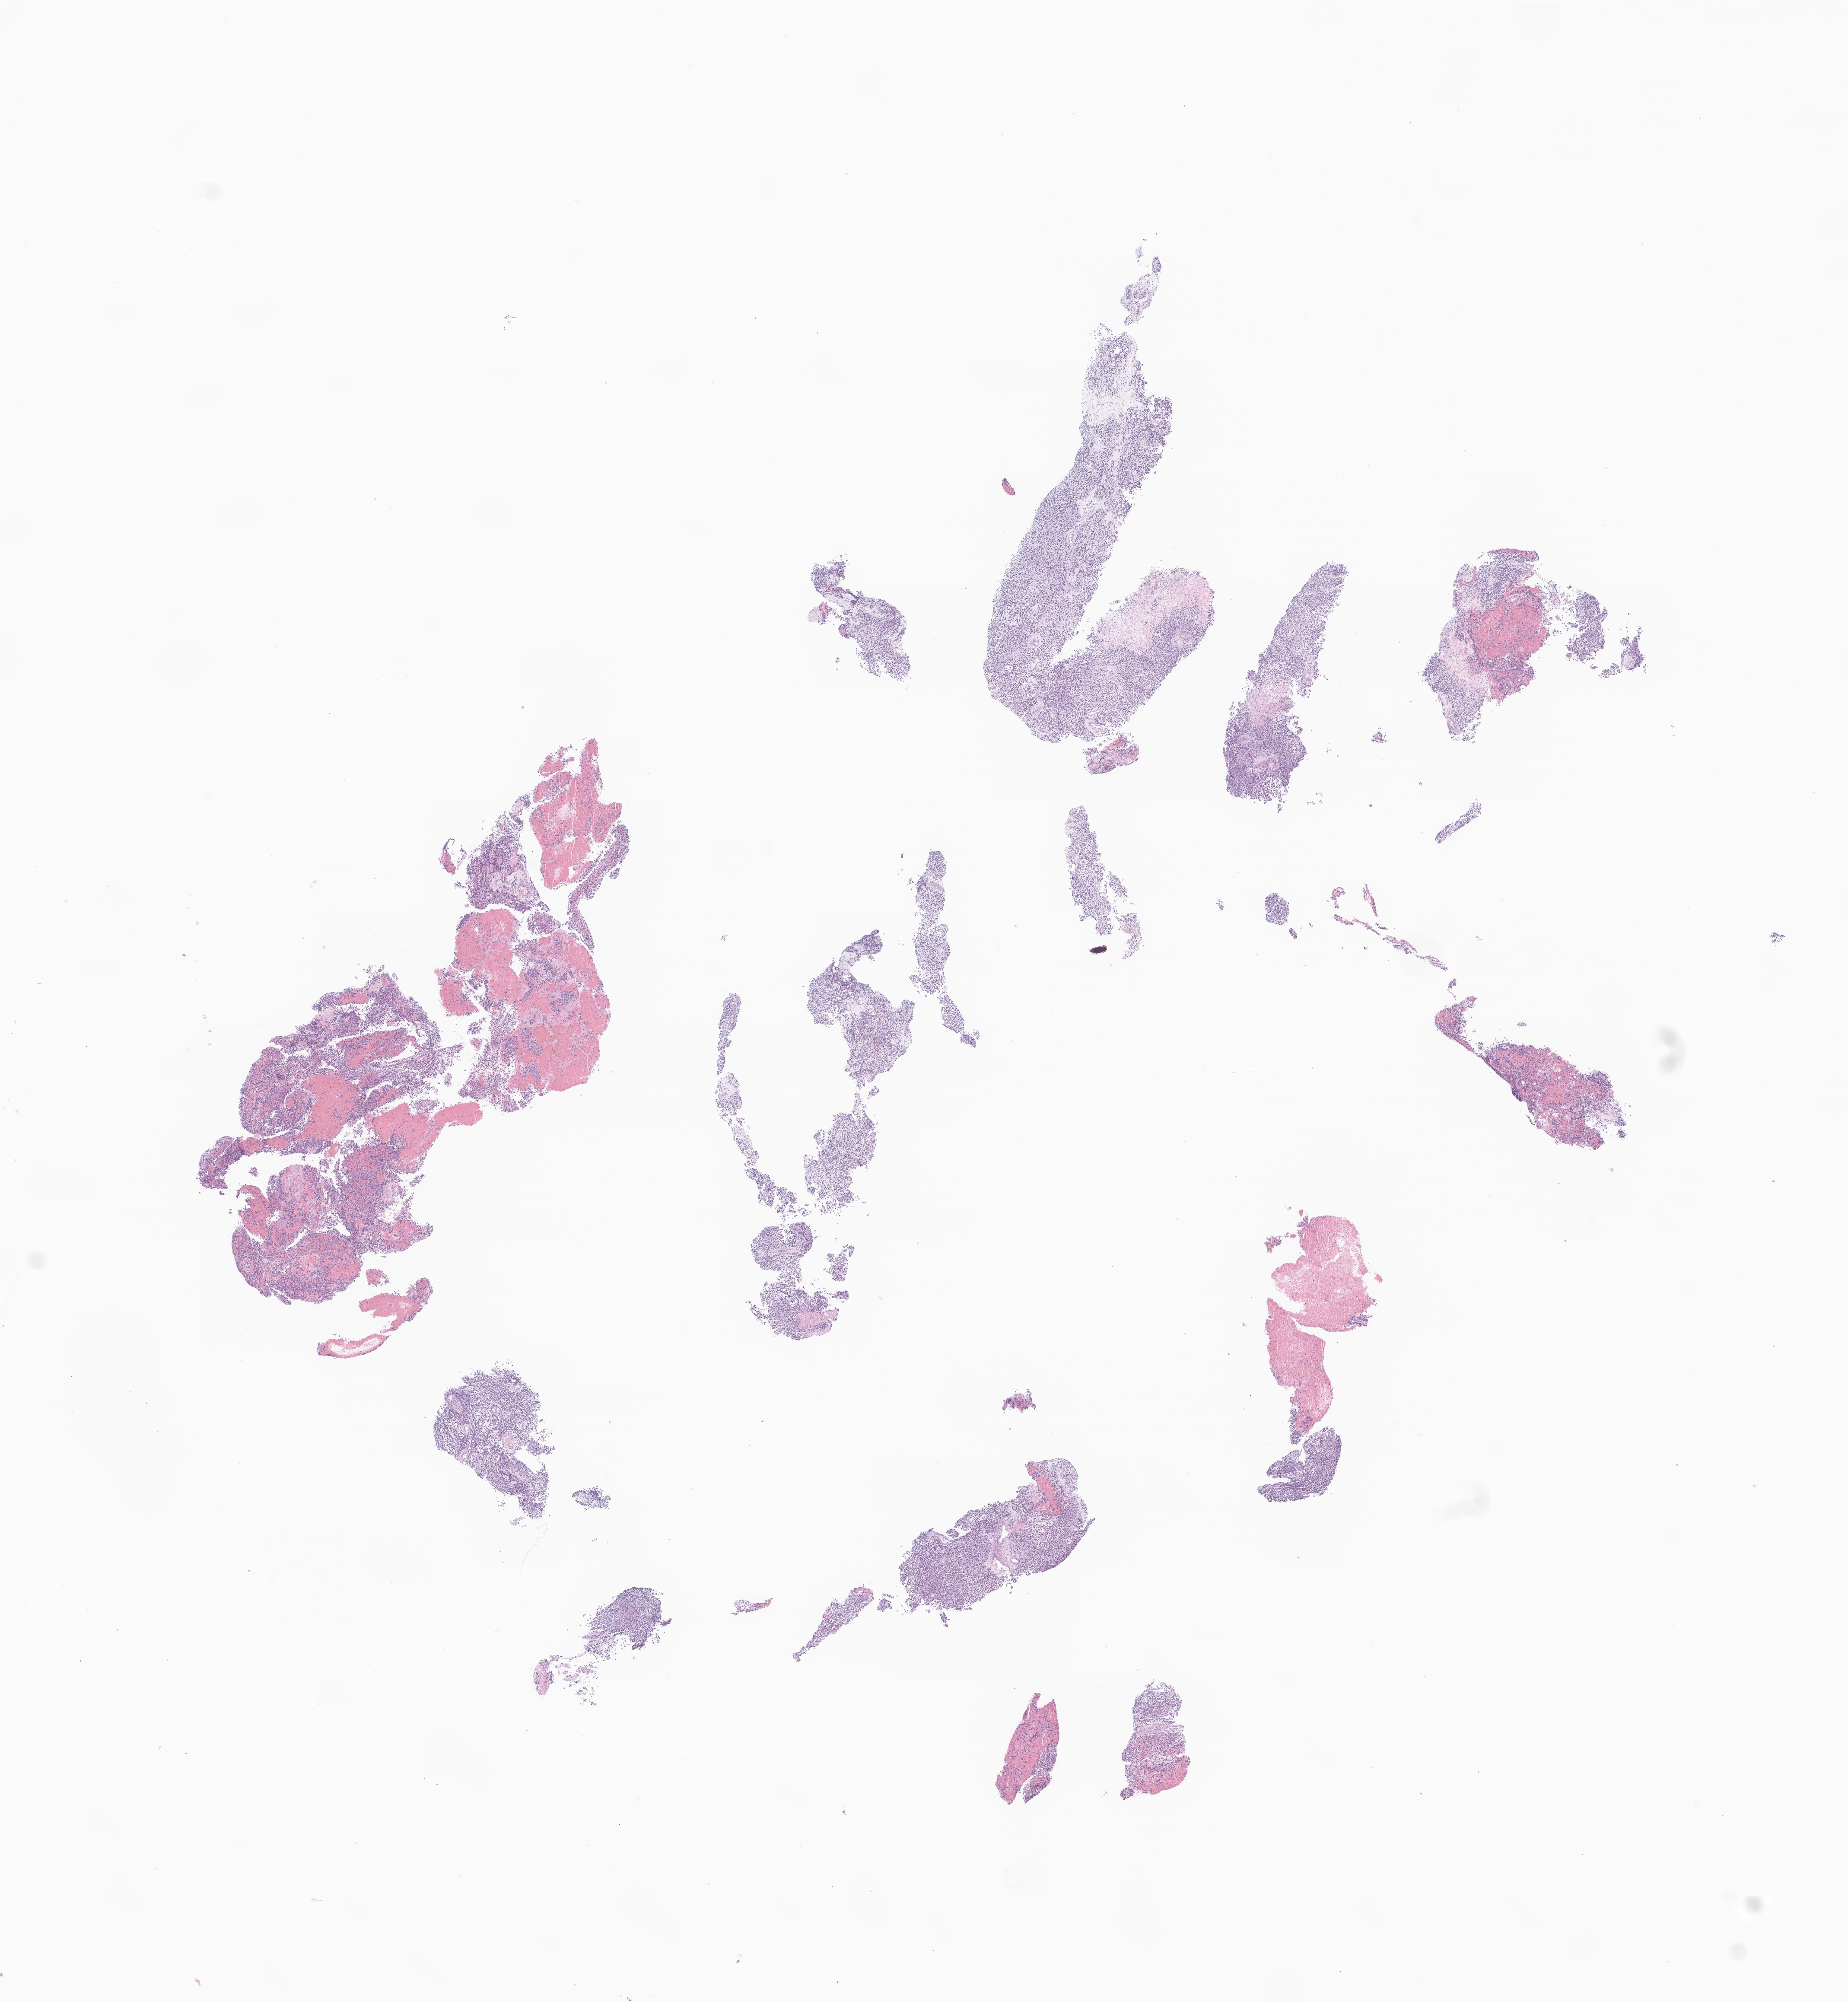
Whole-slide image, haematoxylin and eosin stain of tumor tissue from the soft tissue, a low-resolution overview of the entire scanned area, about 18.0 x 19.5 mm, formalin-fixed, paraffin-embedded (FFPE) tissue. Patient male; age 78 months (6 years 6 months).
Diagnosis (ICD-O-3 morphology term): Rhabdomyoma, NOS.